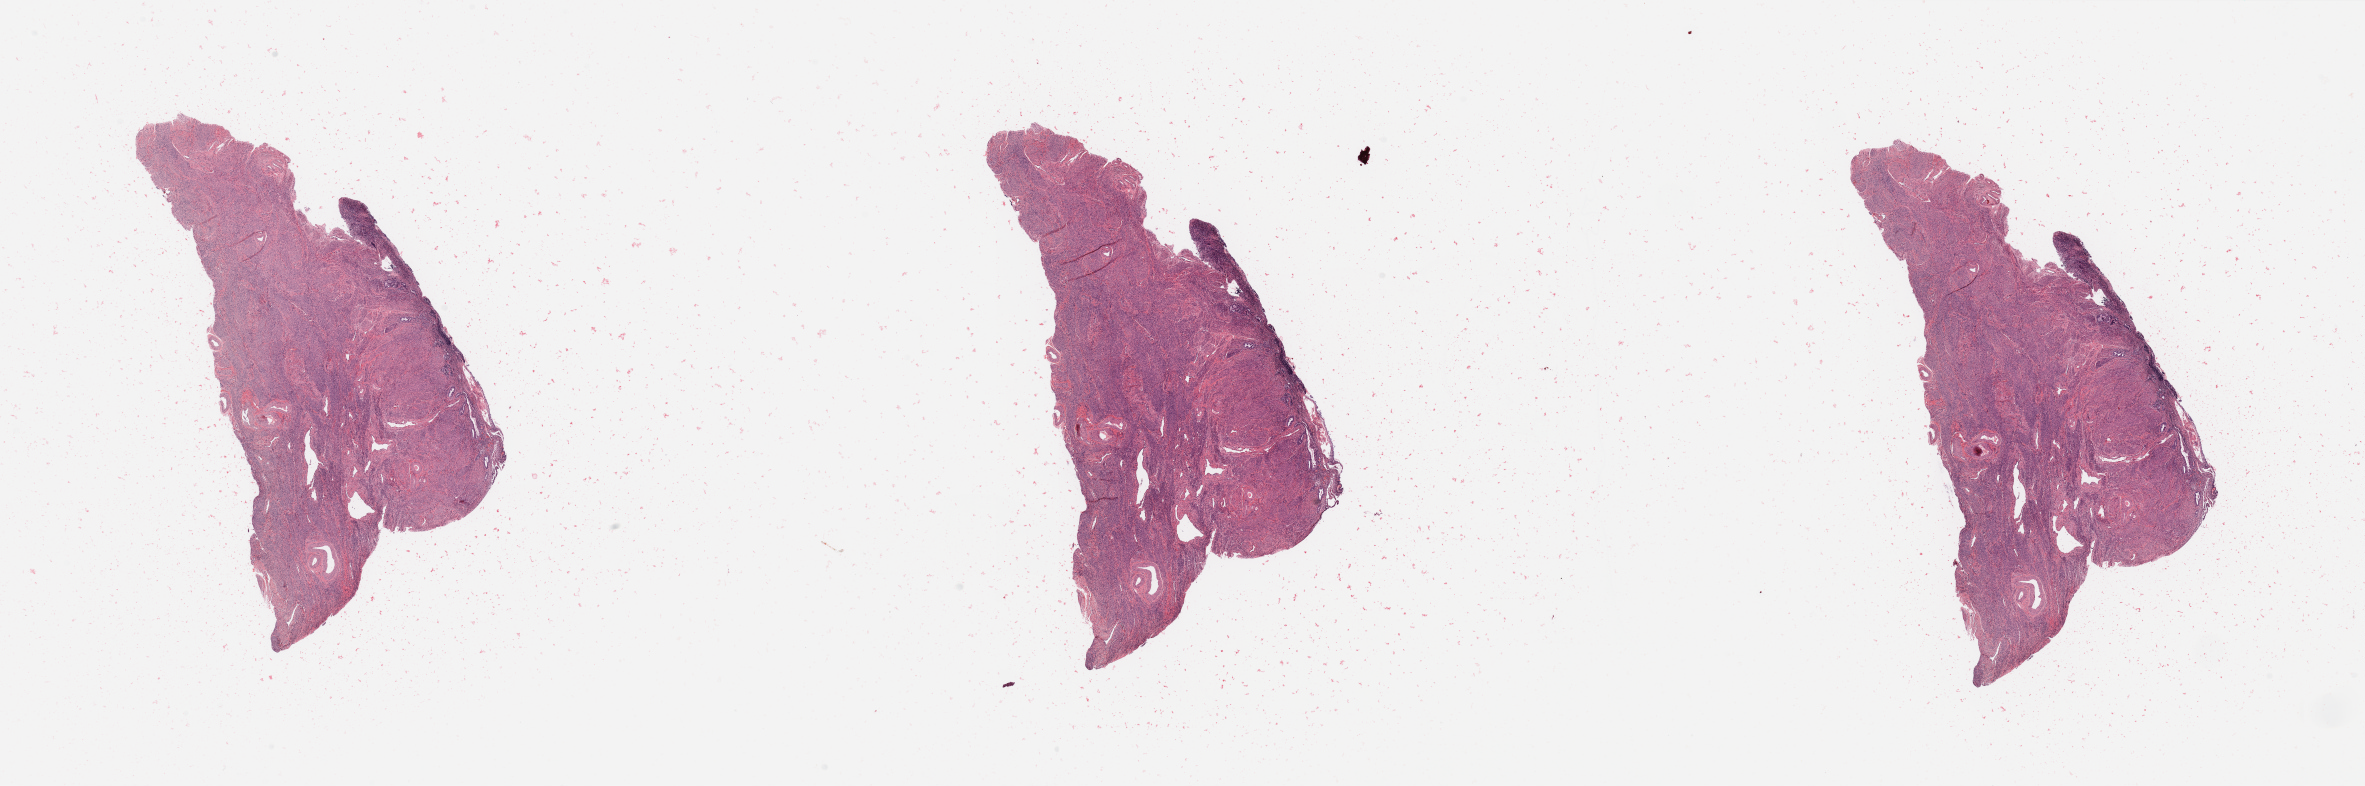
Digitized Hematoxylin and eosin (H&E) stained tissue section (whole slide), shown as a low-resolution overview of the whole scanned area (about 37.4 x 12.4 mm); uterus, normal (non-tumour) tissue. Female, 62 y/o.
This section: normal (non-tumour) tissue from the same patient. Patient diagnosis: Endometrioid adenocarcinoma, NOS.